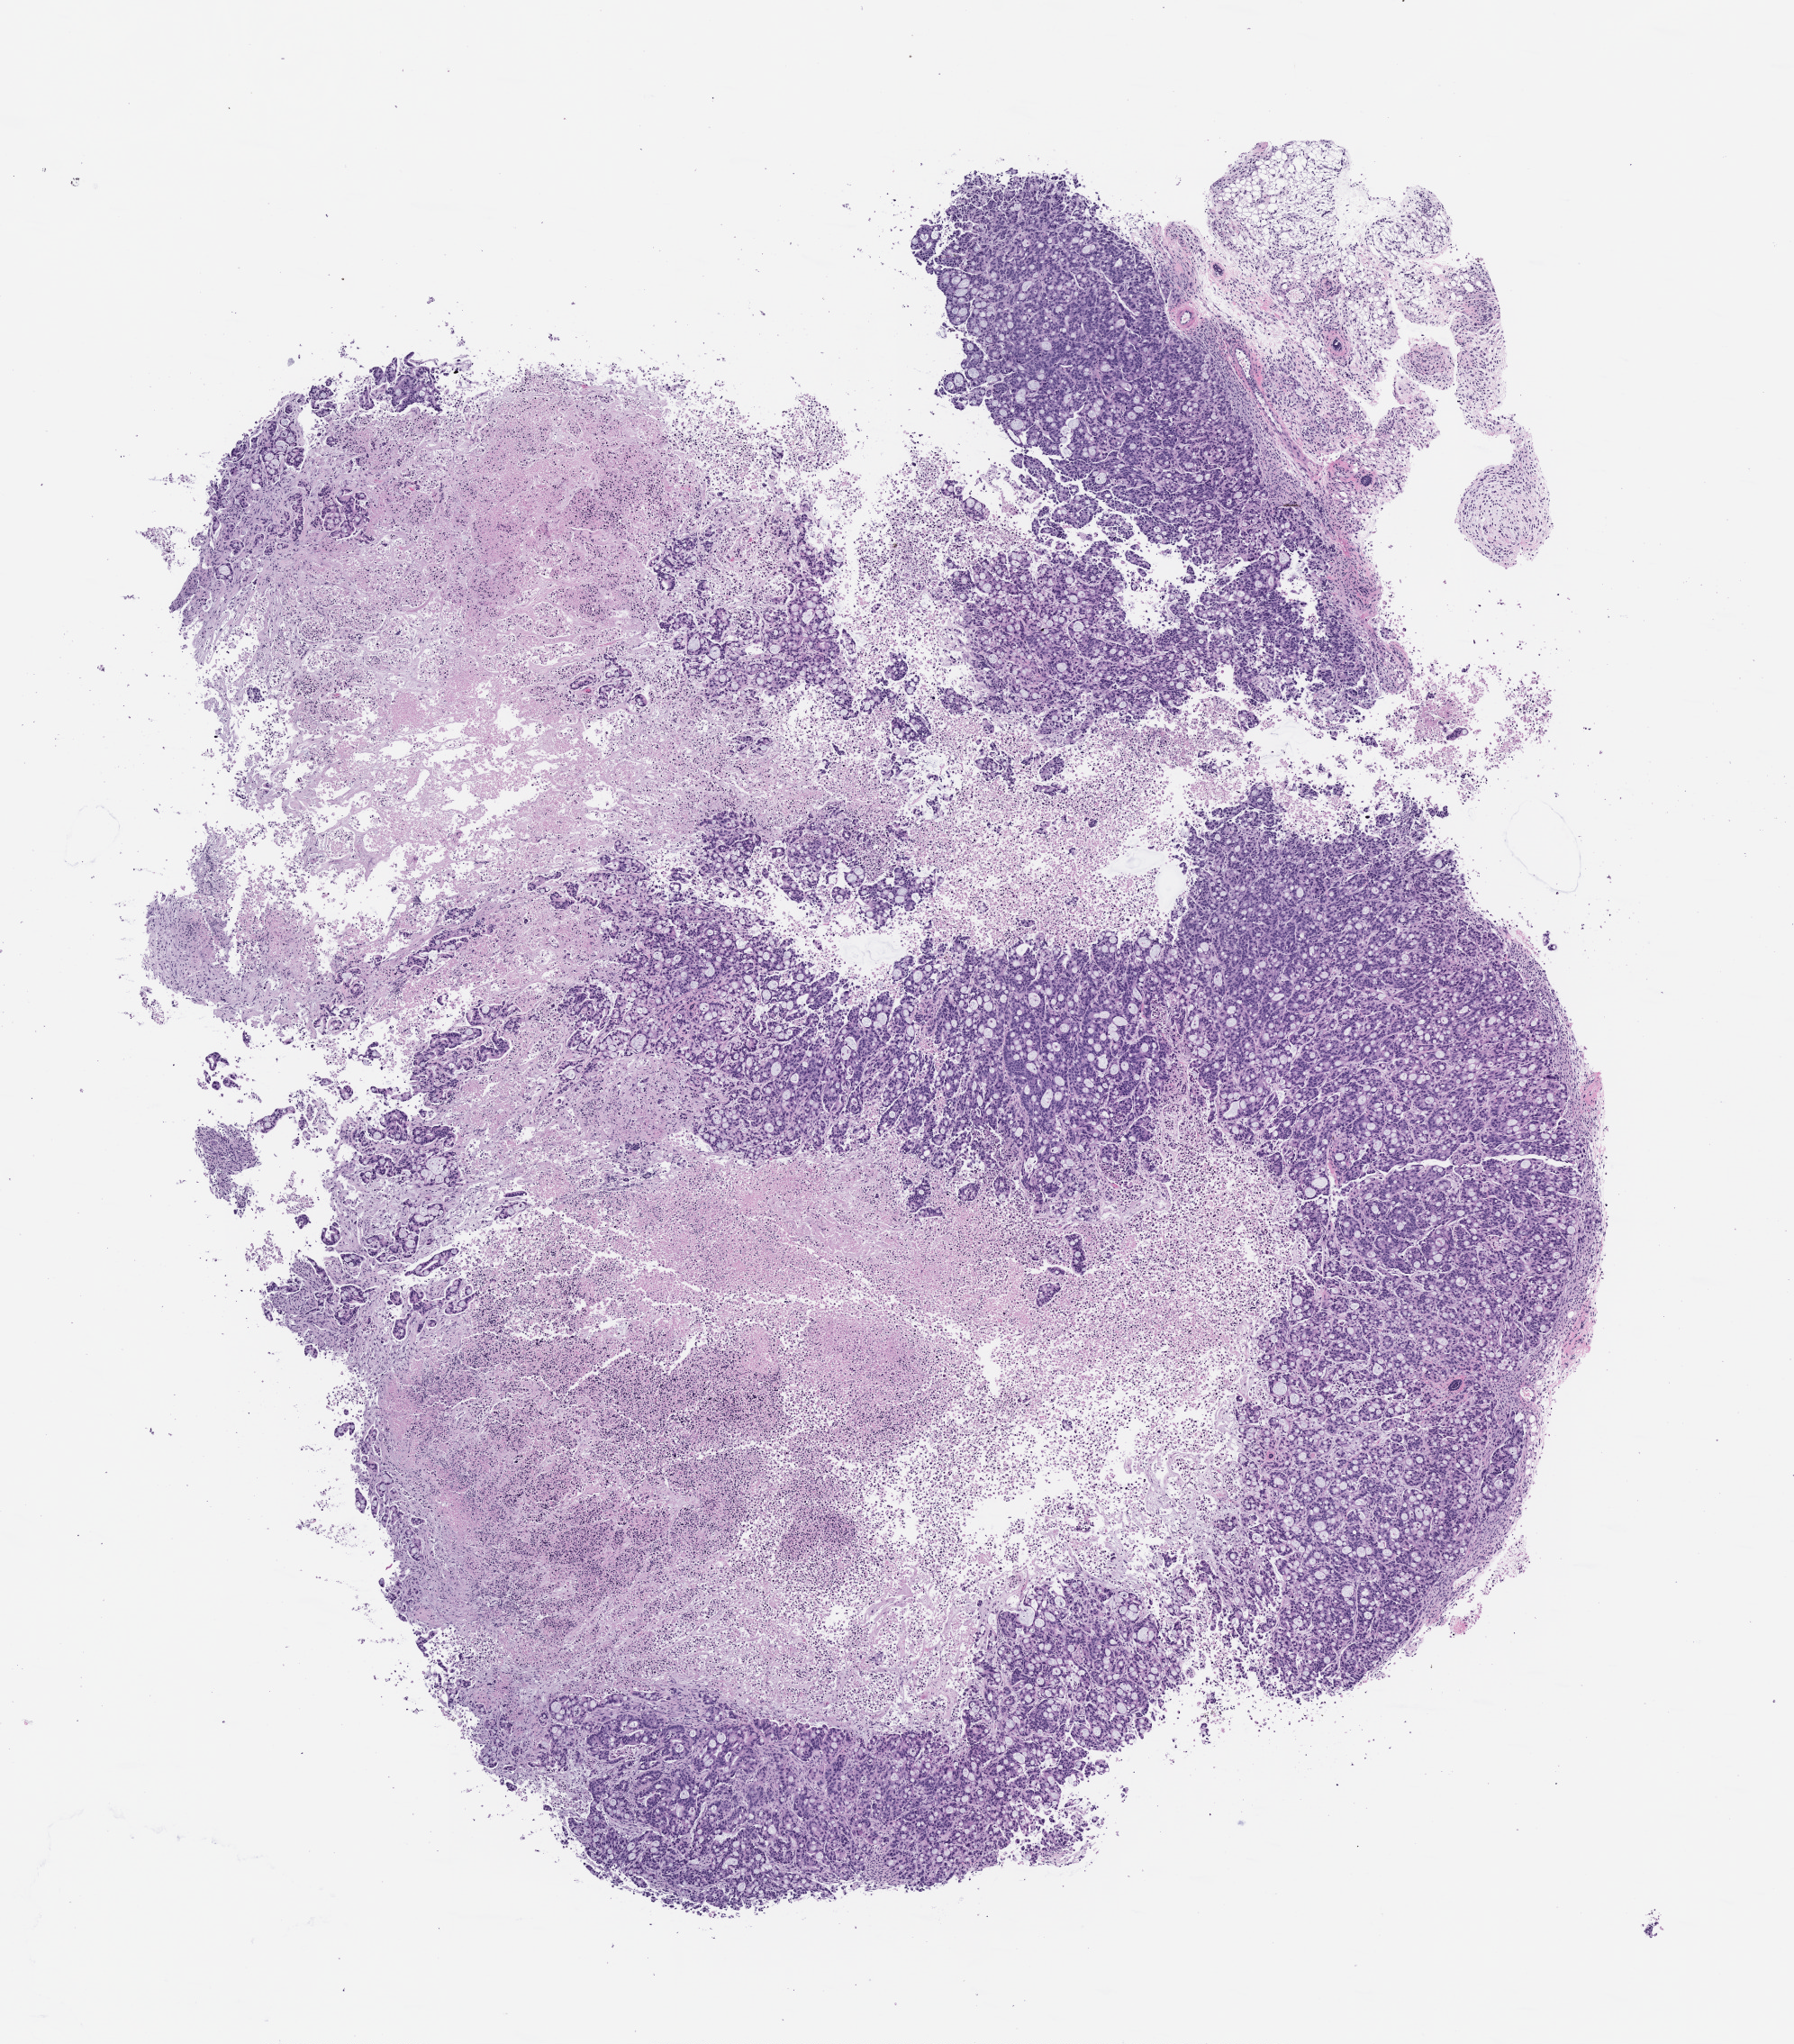
H&E whole-slide image of a patient-derived xenograft (PDX) tumor grown in a mouse, passage 0, whole scanned area (about 8.0 x 9.1 mm) shown as a low-resolution overview; FFPE section; originating tumor site category: colon.
Originating patient diagnosis: Colon Adenocarcinoma.